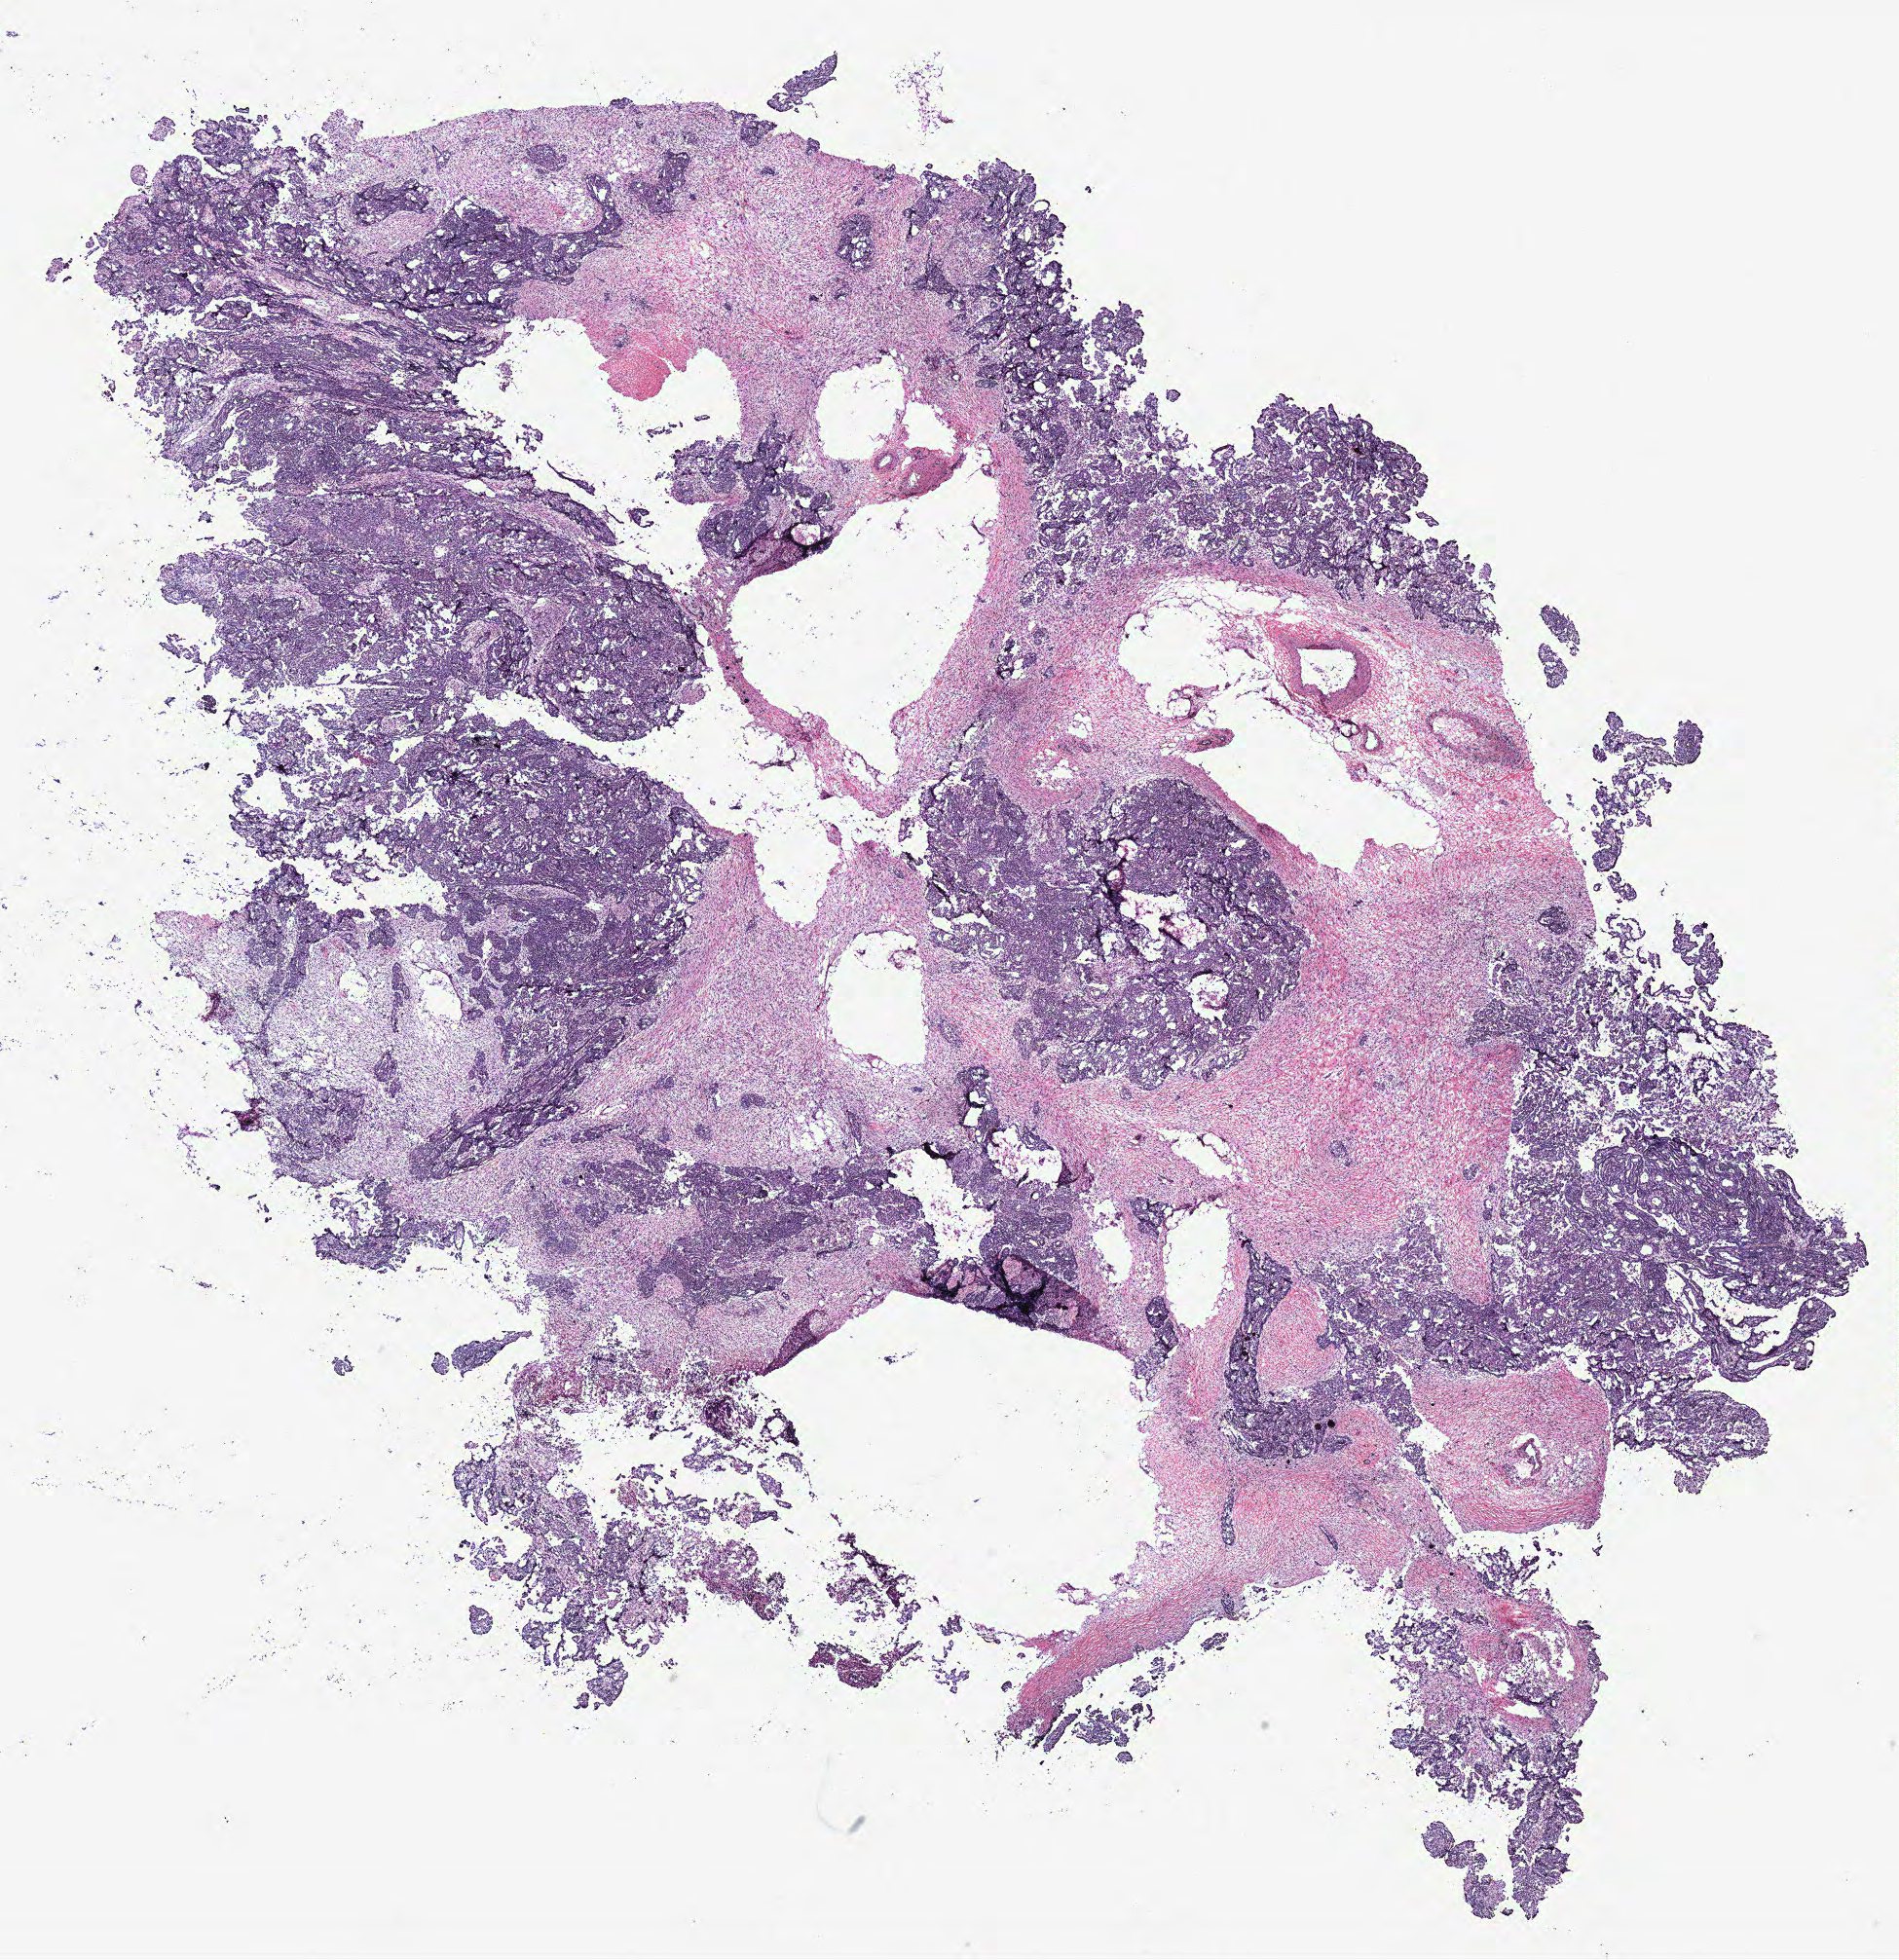
Digitized Hematoxylin and eosin (H&E) stained tissue section (whole slide) — whole scanned area (about 15.6 x 16.1 mm, slide scanned at 40x) shown as a low-resolution overview. Tumour tissue sample, ovary. Female, 59 y/o.
* histologic diagnosis: Serous adenocarcinoma, NOS
* primary tumour site (as recorded): fallopian tube